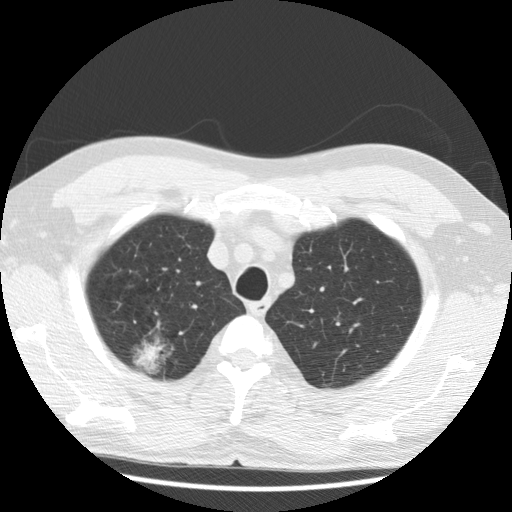
Low-dose screening chest CT, one axial slice. Slice 99 of 122 in the series (ordered by position). 120 kVp. Lung window (W 1500 / L -600 HU). 512 × 512 image matrix, field of view 350 × 350 mm.
Outlined on this slice (manually delineated by an expert):
- lesion 1 (tumor, upper lobe of right lung): bounding box <137,344,160,368> (left, top, right, bottom; pixels)